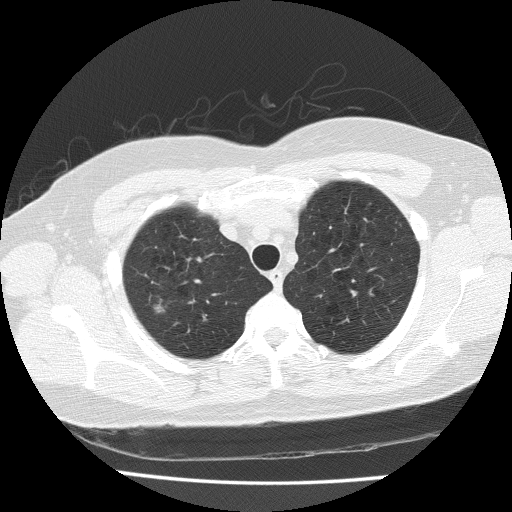
Low-dose screening chest CT, axial slice. Baseline screening round. Lung window (W 1500 / L -600 HU). 2 mm slice thickness. Lung (sharp) reconstruction kernel (FC51). 512 × 512 image matrix. Female participant, aged 57 years at enrolment. Former smoker at enrolment.
• Expert-annotated lung lesion, box from (x=139, y=293) to (x=179, y=327) px.
• The exam's reader record, not a measurement of the box and not confirmed to be the same lesion: non-calcified nodule or mass ≥4 mm, right upper lobe, 8 × 7 mm, spiculated (stellate) margins, soft tissue attenuation.